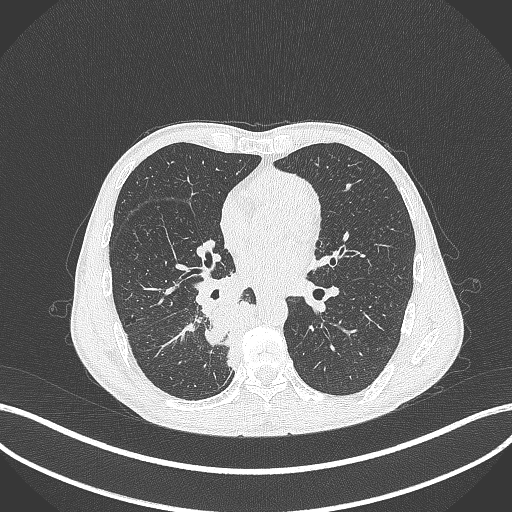
Chest CT, one axial slice; position 182 of 371 along the scan axis; 120 kVp; lung window (W 1500 / L -600 HU); 1 mm slice thickness; 512 × 512 image matrix, field of view 400 × 400 mm. Male patient, age 58 years. From the clinical record (not read from this slice): clinical TNM (as recorded): T3 N1 M1.
Structures marked on this image (rectangle marked by the reading radiologist):
- lung tumour (recorded histology: squamous cell carcinoma): bounding box (x1, y1, x2, y2) in pixels: (193, 296, 257, 374)